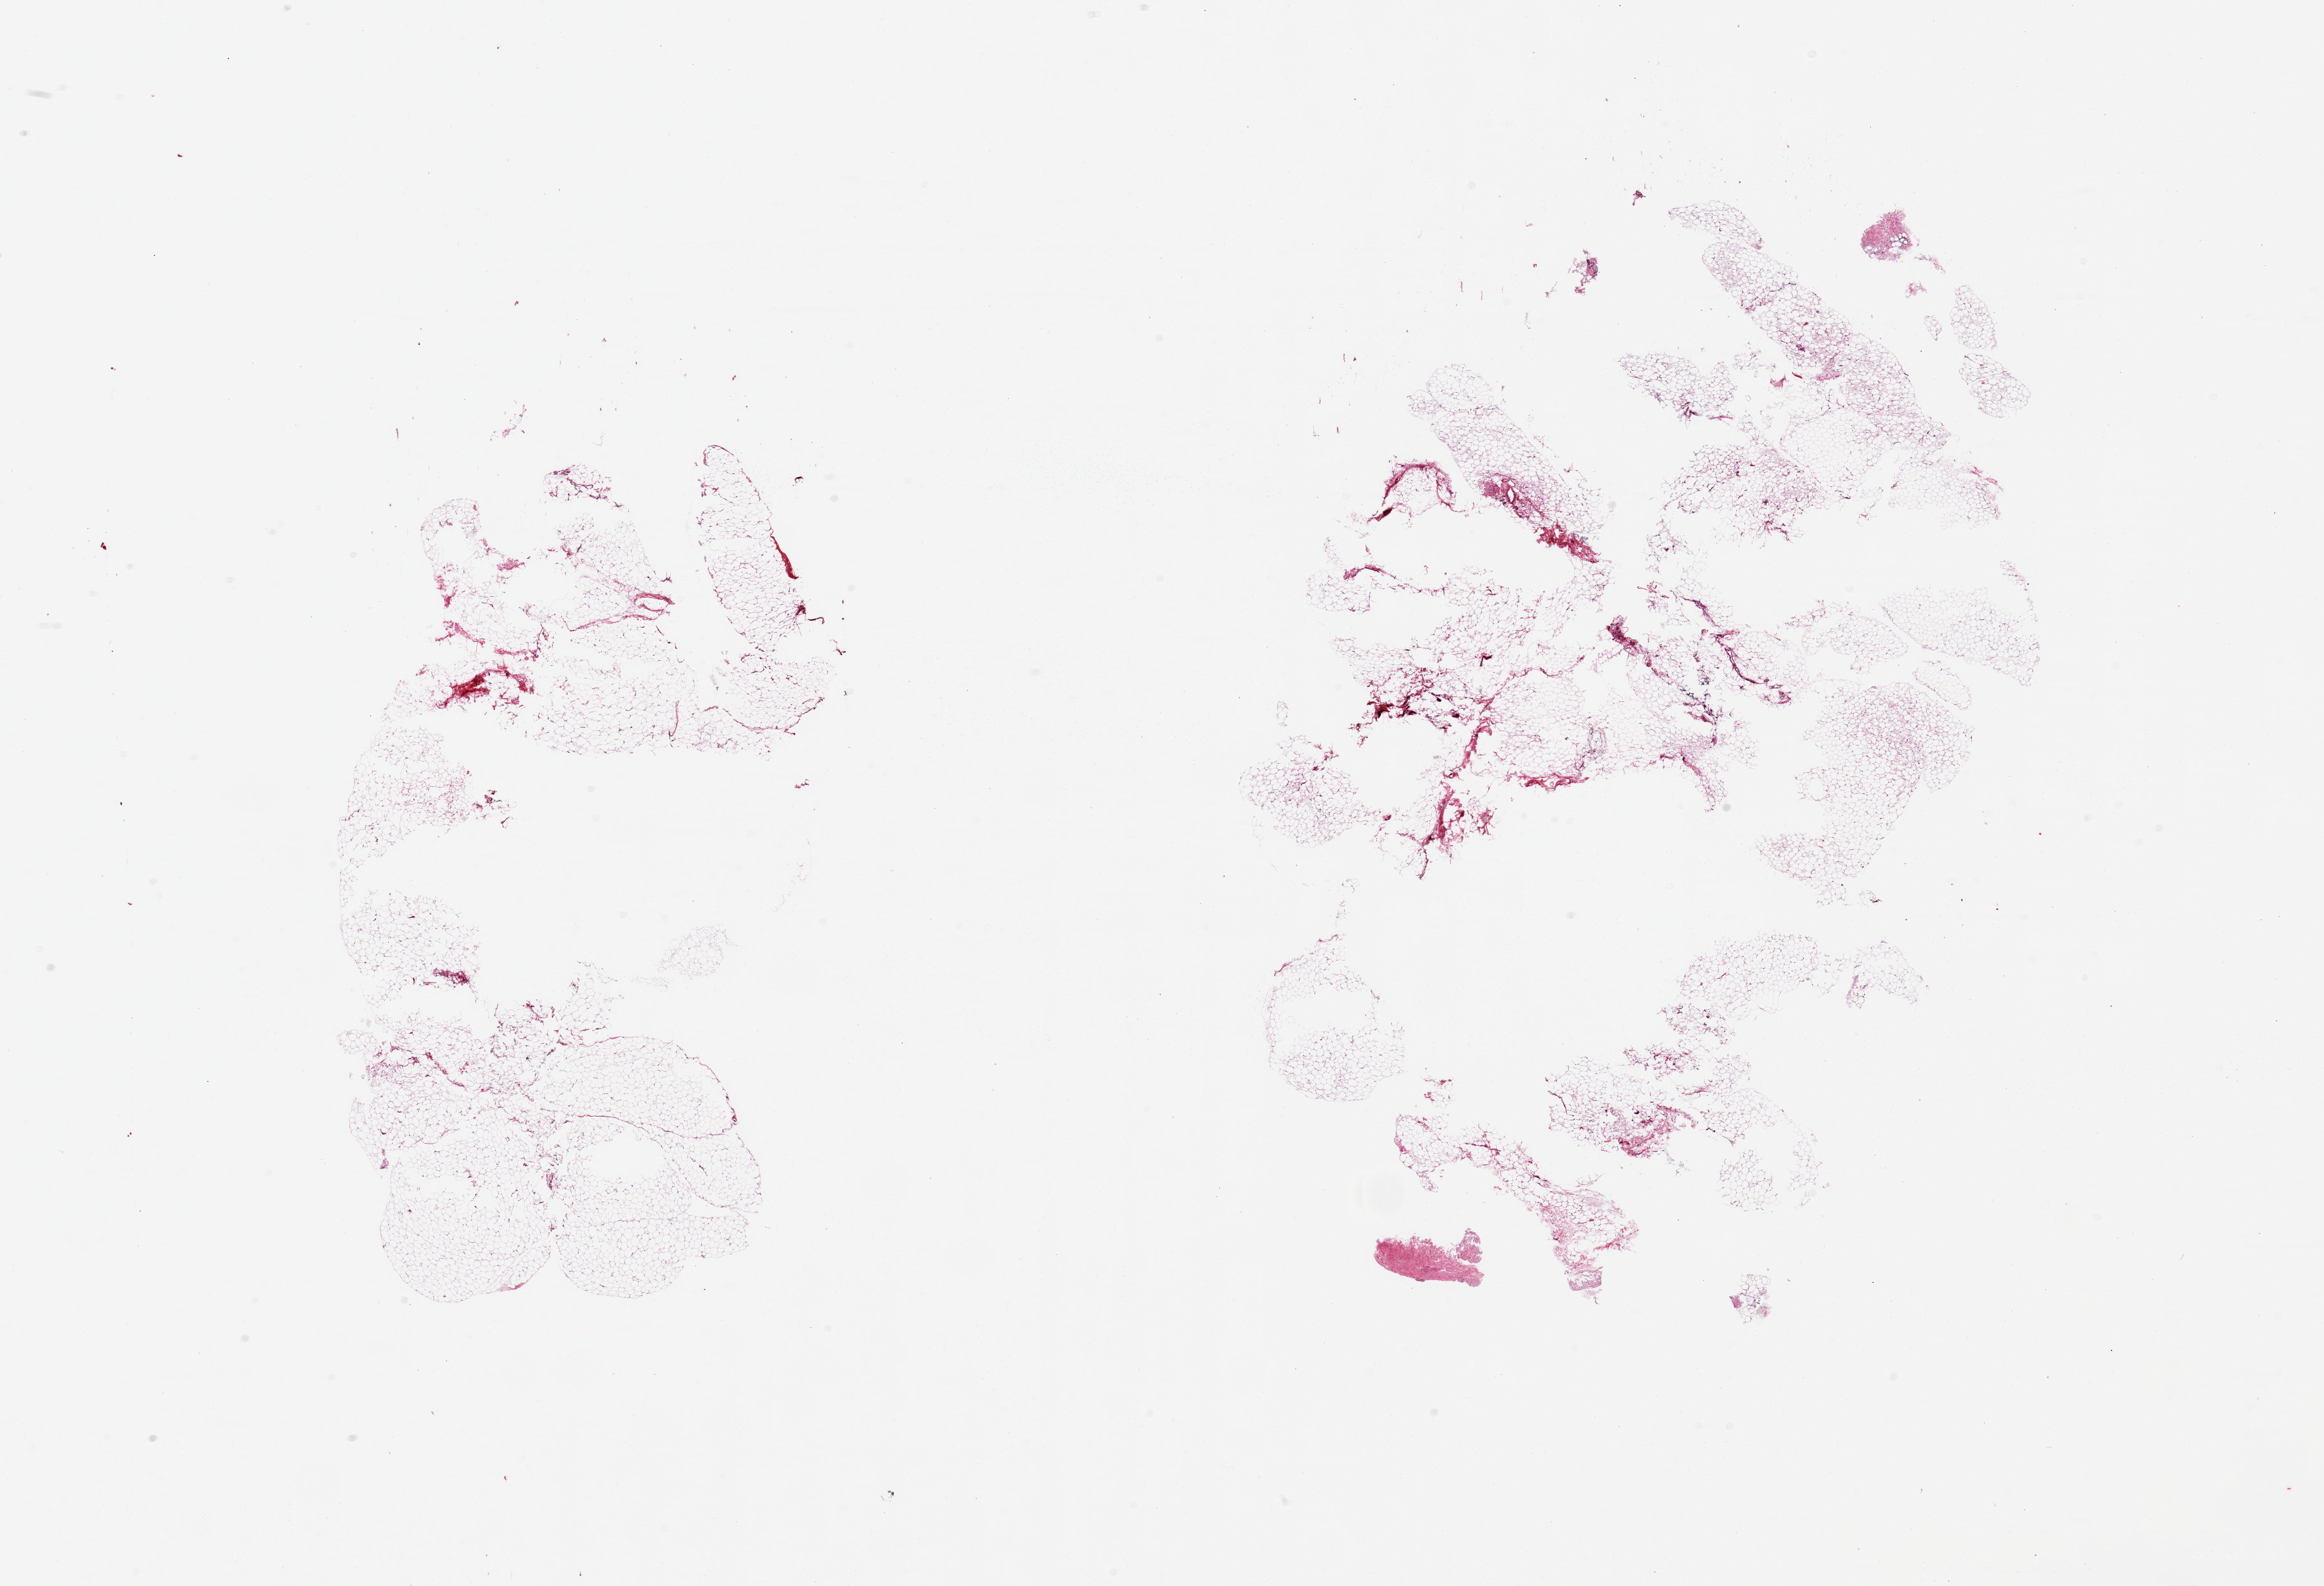
Haematoxylin and eosin whole-slide image, brightfield, whole scanned area (about 28.5 x 19.5 mm, from a 20x scan) shown as a low-resolution overview. PAXgene-fixed paraffin-embedded (PFPE) section. Sampled site (target tissue): omentum. Donor tissue sample. Donor: male.
• reviewer comment on this tissue sample: 2 pieces, trace interstitial fat